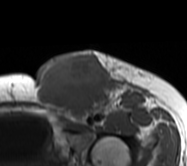
MRI of an extremity soft-tissue mass, one axial slice. Slice 40 of 62 in the series (ordered by position). MR volume resampled by the dataset authors to the PET/CT grid (not the native acquisition matrix). 3.27 mm slice thickness. 187 × 166 image matrix, field of view 183 × 162 mm. Female patient. From the clinical record (not read from this slice): histological type: leiomyosarcoma; grade: high; site of the primary tumour: groin.
Structures marked on this image (expert contour drawn on MRI and transferred to this co-registered scan by the dataset authors):
- gross tumour volume including surrounding oedema: bounding box <34,50,149,125> (left, top, right, bottom; pixels)
- gross tumour volume (mass): <34,53,115,121>